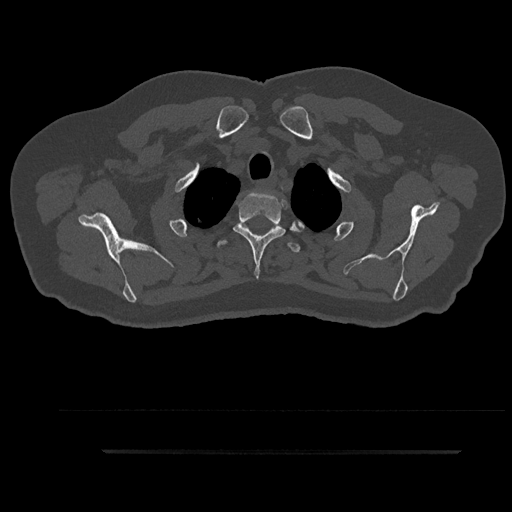
CT including the spine, one axial slice; slice 753 of 797 in the series (ordered by position); reconstruction kernel Br40s/3; 120 kVp; bone window (W 1800 / L 400 HU); 512 × 512 image matrix, field of view 432 × 432 mm. Male patient, age 63 years. Case-level facts recorded for this patient, not image findings: primary cancer: renal; vertebrae with lytic lesions (as recorded): T8.
Outlined on this slice (semi-automatically segmented with operator editing):
- T2 vertebra: bounding box [x1, y1, x2, y2] px = [233, 191, 303, 278]
- T3 vertebra: [217, 222, 301, 253]